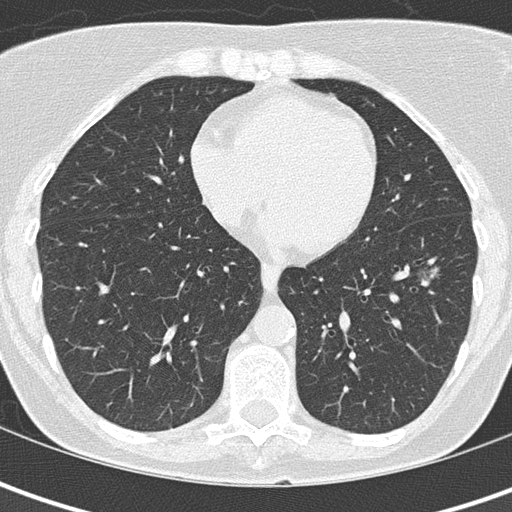
Chest CT (low-dose screening protocol), one axial image; first (baseline) screen; lung window (W 1500 / L -600 HU); 2 mm slice thickness; lung (sharp) reconstruction kernel (B50f). Female, age 61 years at enrolment.
- Lesion marked by an expert reader, box from (x=378, y=247) to (x=453, y=304) px.
- The exam's reader record, not a measurement of the box and not confirmed to be the same lesion: non-calcified nodule or mass ≥4 mm, left lower lobe, 29 × 16 mm, ground glass attenuation.
- Official screen result: positive, change unspecified: nodule(s) >= 4 mm or enlarging nodule(s), mass(es), or other non-specific abnormalities suspicious for lung cancer.
- Lung cancer was diagnosed 259 days after this screen: bronchiolo-alveolar adenocarcinoma, NOS, left lower lobe, well differentiated (G1), stage IA (AJCC 6th edition), 10 mm at pathology.